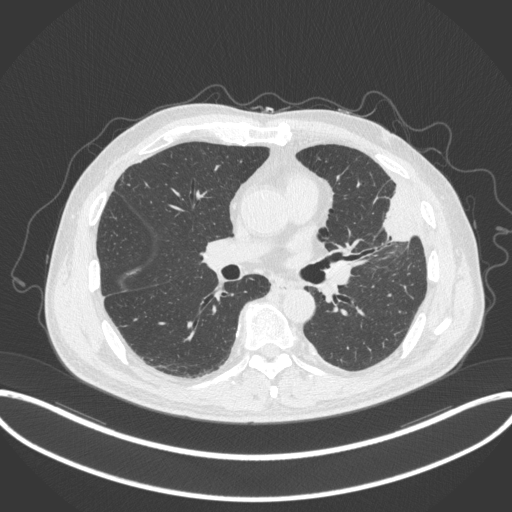
Chest CT, one axial slice. Position 178 of 382 along the scan axis. 120 kVp. Lung window (W 1500 / L -600 HU). 1 mm slice thickness. 512 × 512 image matrix, field of view 415 × 415 mm. Patient: male, 64 years. From the clinical record (not read from this slice): clinical TNM (as recorded): T4 N1 M0; histopathological grade: G3.
Outlined on this slice (bounding box drawn by a radiologist):
- lung tumour (recorded histology: adenocarcinoma): box from (x=373, y=184) to (x=417, y=246) px